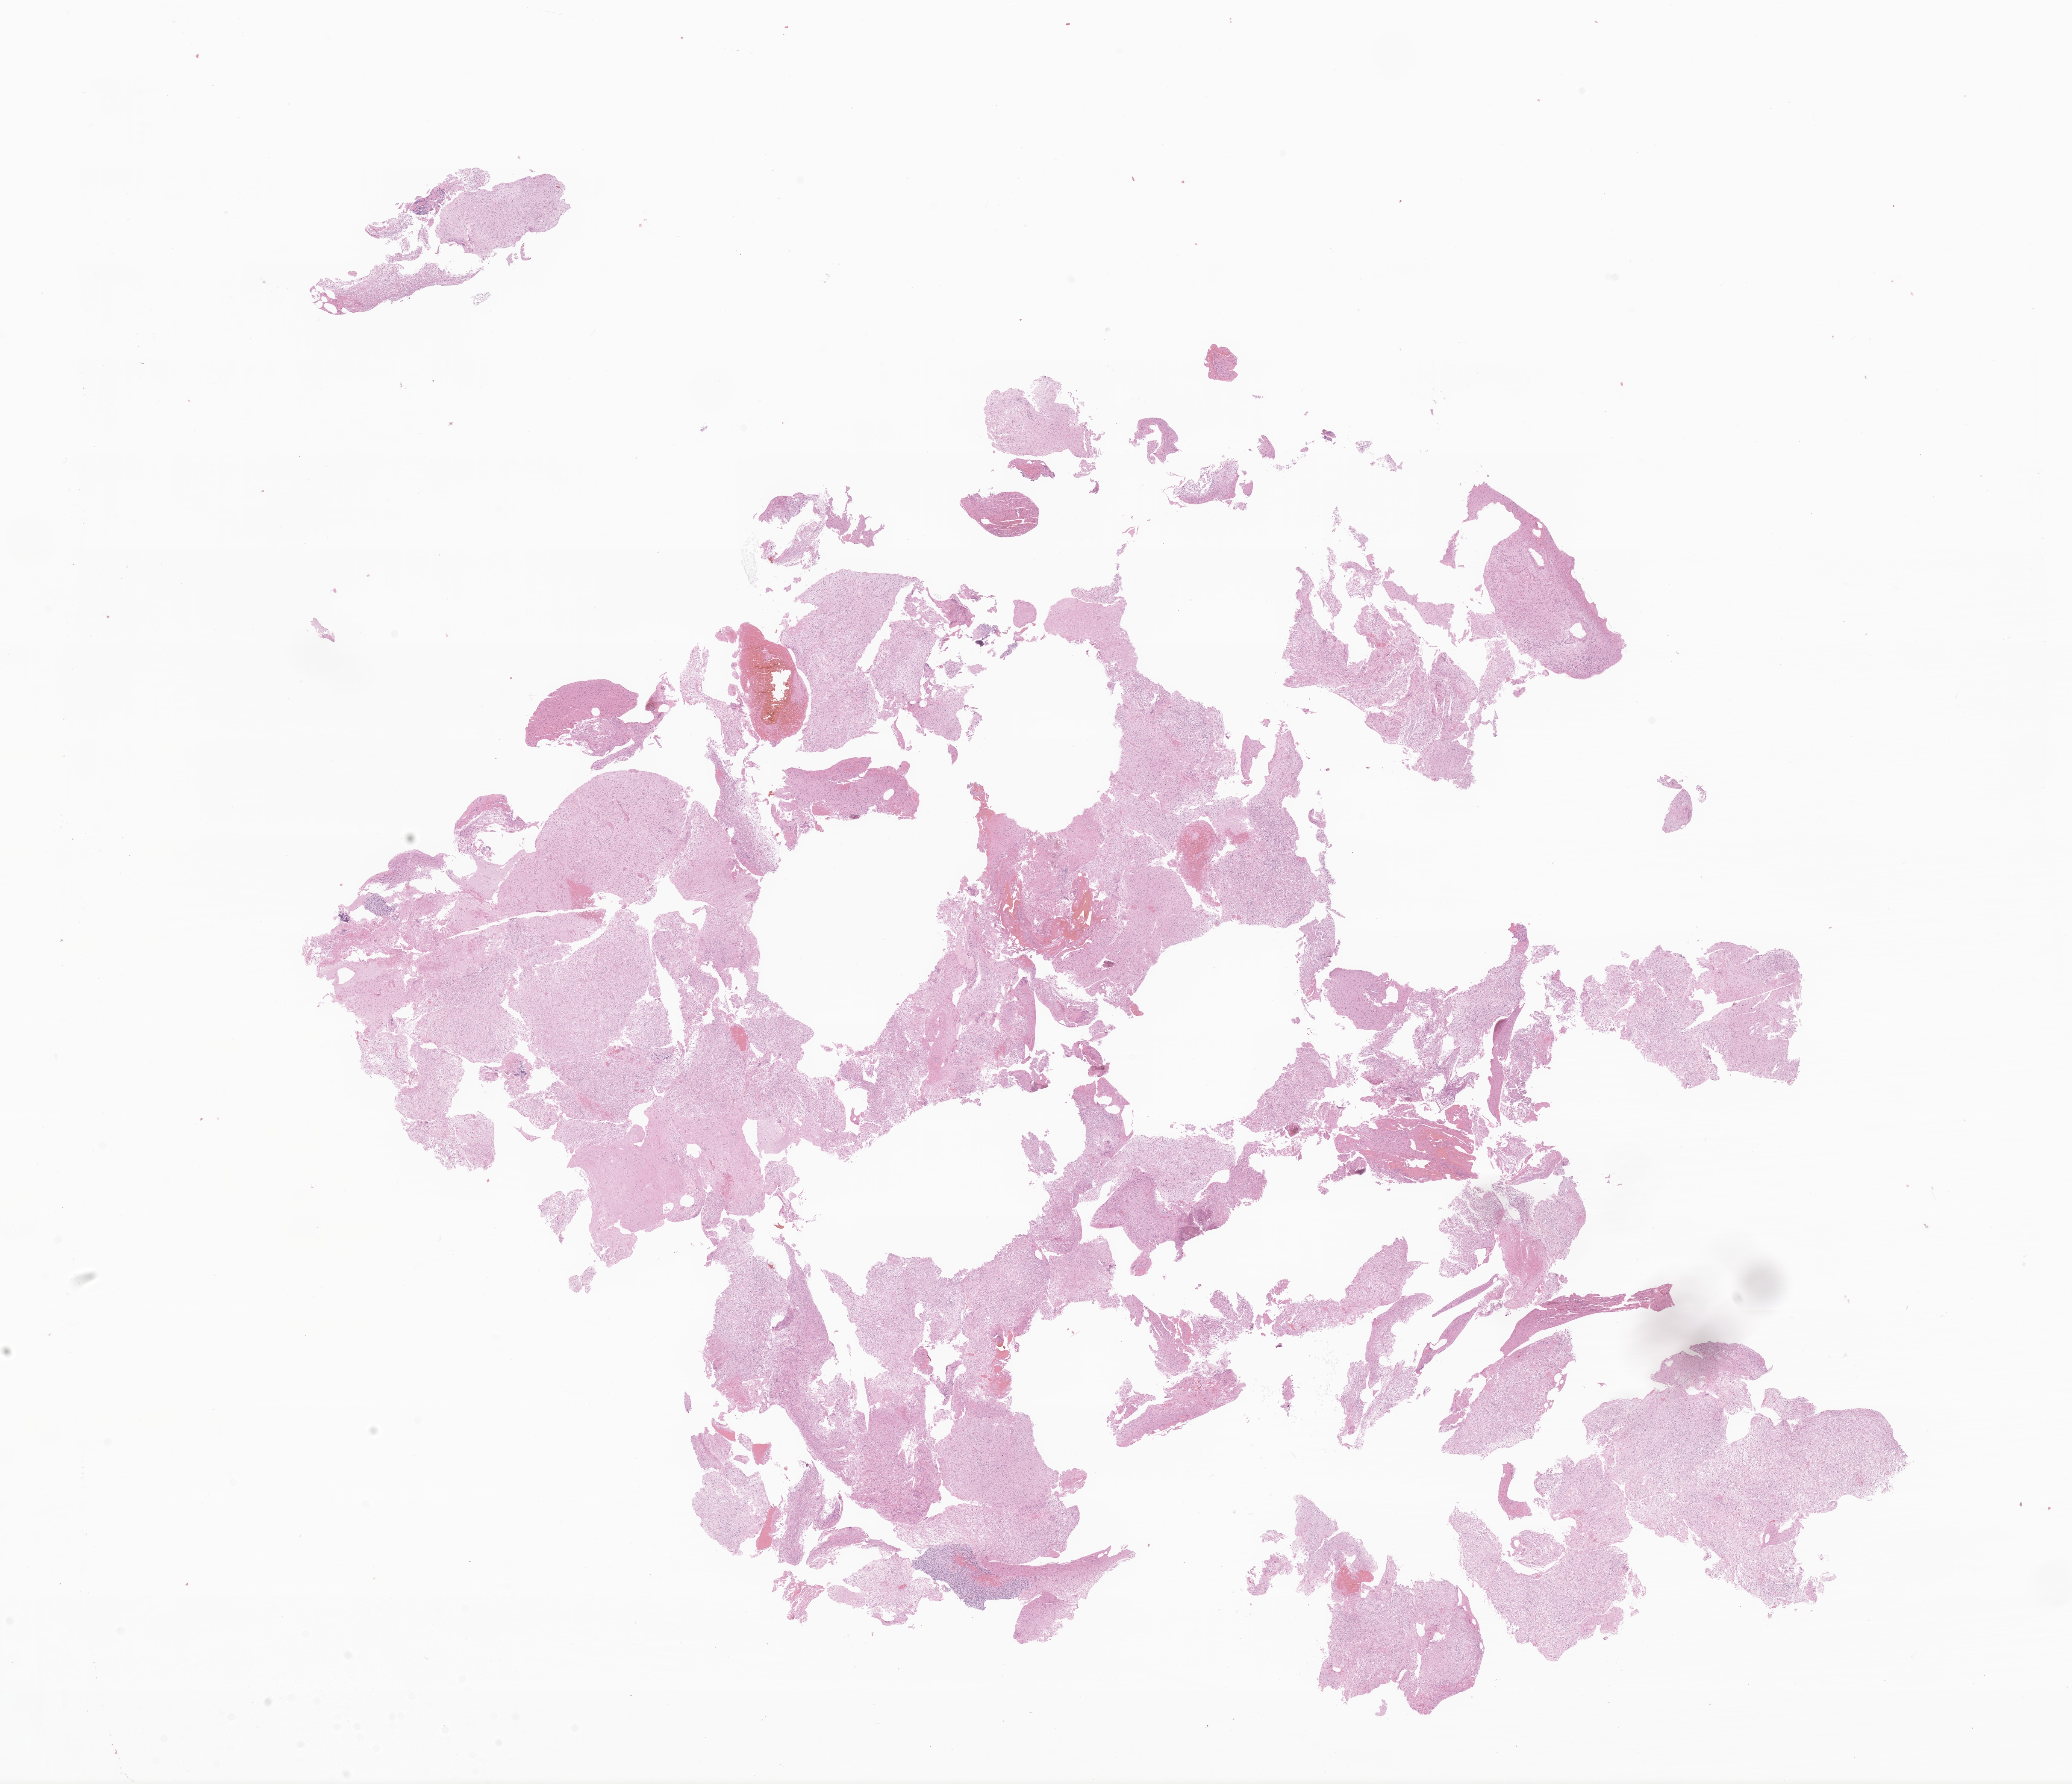
Digitized haematoxylin and eosin-stained section of tumor tissue from the brain, low-resolution overview of the scanned area, about 23.2 x 20.0 mm, formalin-fixed paraffin-embedded section. Female patient, age 216 months.
Diagnosis: Neoplasm, malignant.